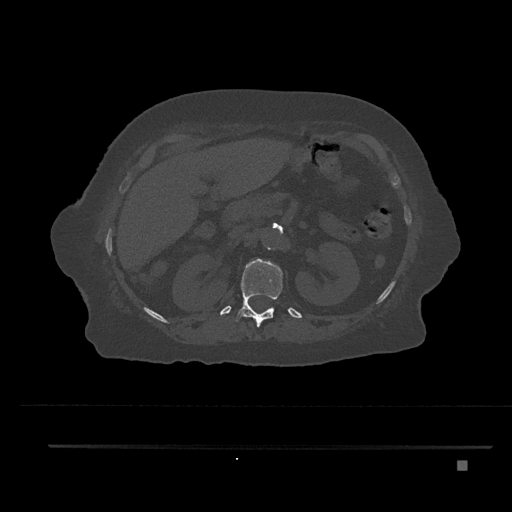
CT including the spine, one axial slice. Position 259 of 797 along the scan axis. 120 kVp. Bone window (W 1800 / L 400 HU). 512 × 512 image matrix, field of view 437 × 437 mm. Patient: female, 76 years. From the clinical record (not read from this slice): primary cancer: lung.
Structures marked on this image (semi-automatic segmentation, software-assisted and operator-edited):
- T12 vertebra: bounding box <235,258,282,327> (left, top, right, bottom; pixels)